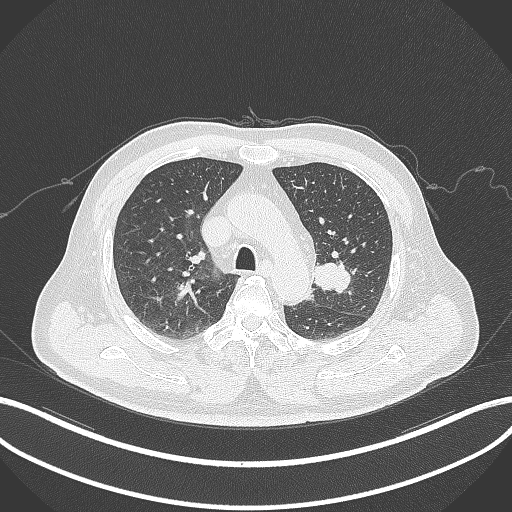
Chest CT, one axial slice; position 213 of 286 along the scan axis; reconstruction kernel B70f; 120 kVp; lung window (W 1500 / L -600 HU); 1 mm slice thickness; 512 × 512 image matrix, field of view 400 × 400 mm. Male patient, age 67 years. Case-level facts recorded for this patient, not image findings: clinical TNM (as recorded): T2a N1 M0; histopathological grade: G3.
Outlined on this slice (bounding box drawn by a radiologist):
- lung tumour (recorded histology: adenocarcinoma): bounding box <310,259,353,293> (left, top, right, bottom; pixels)